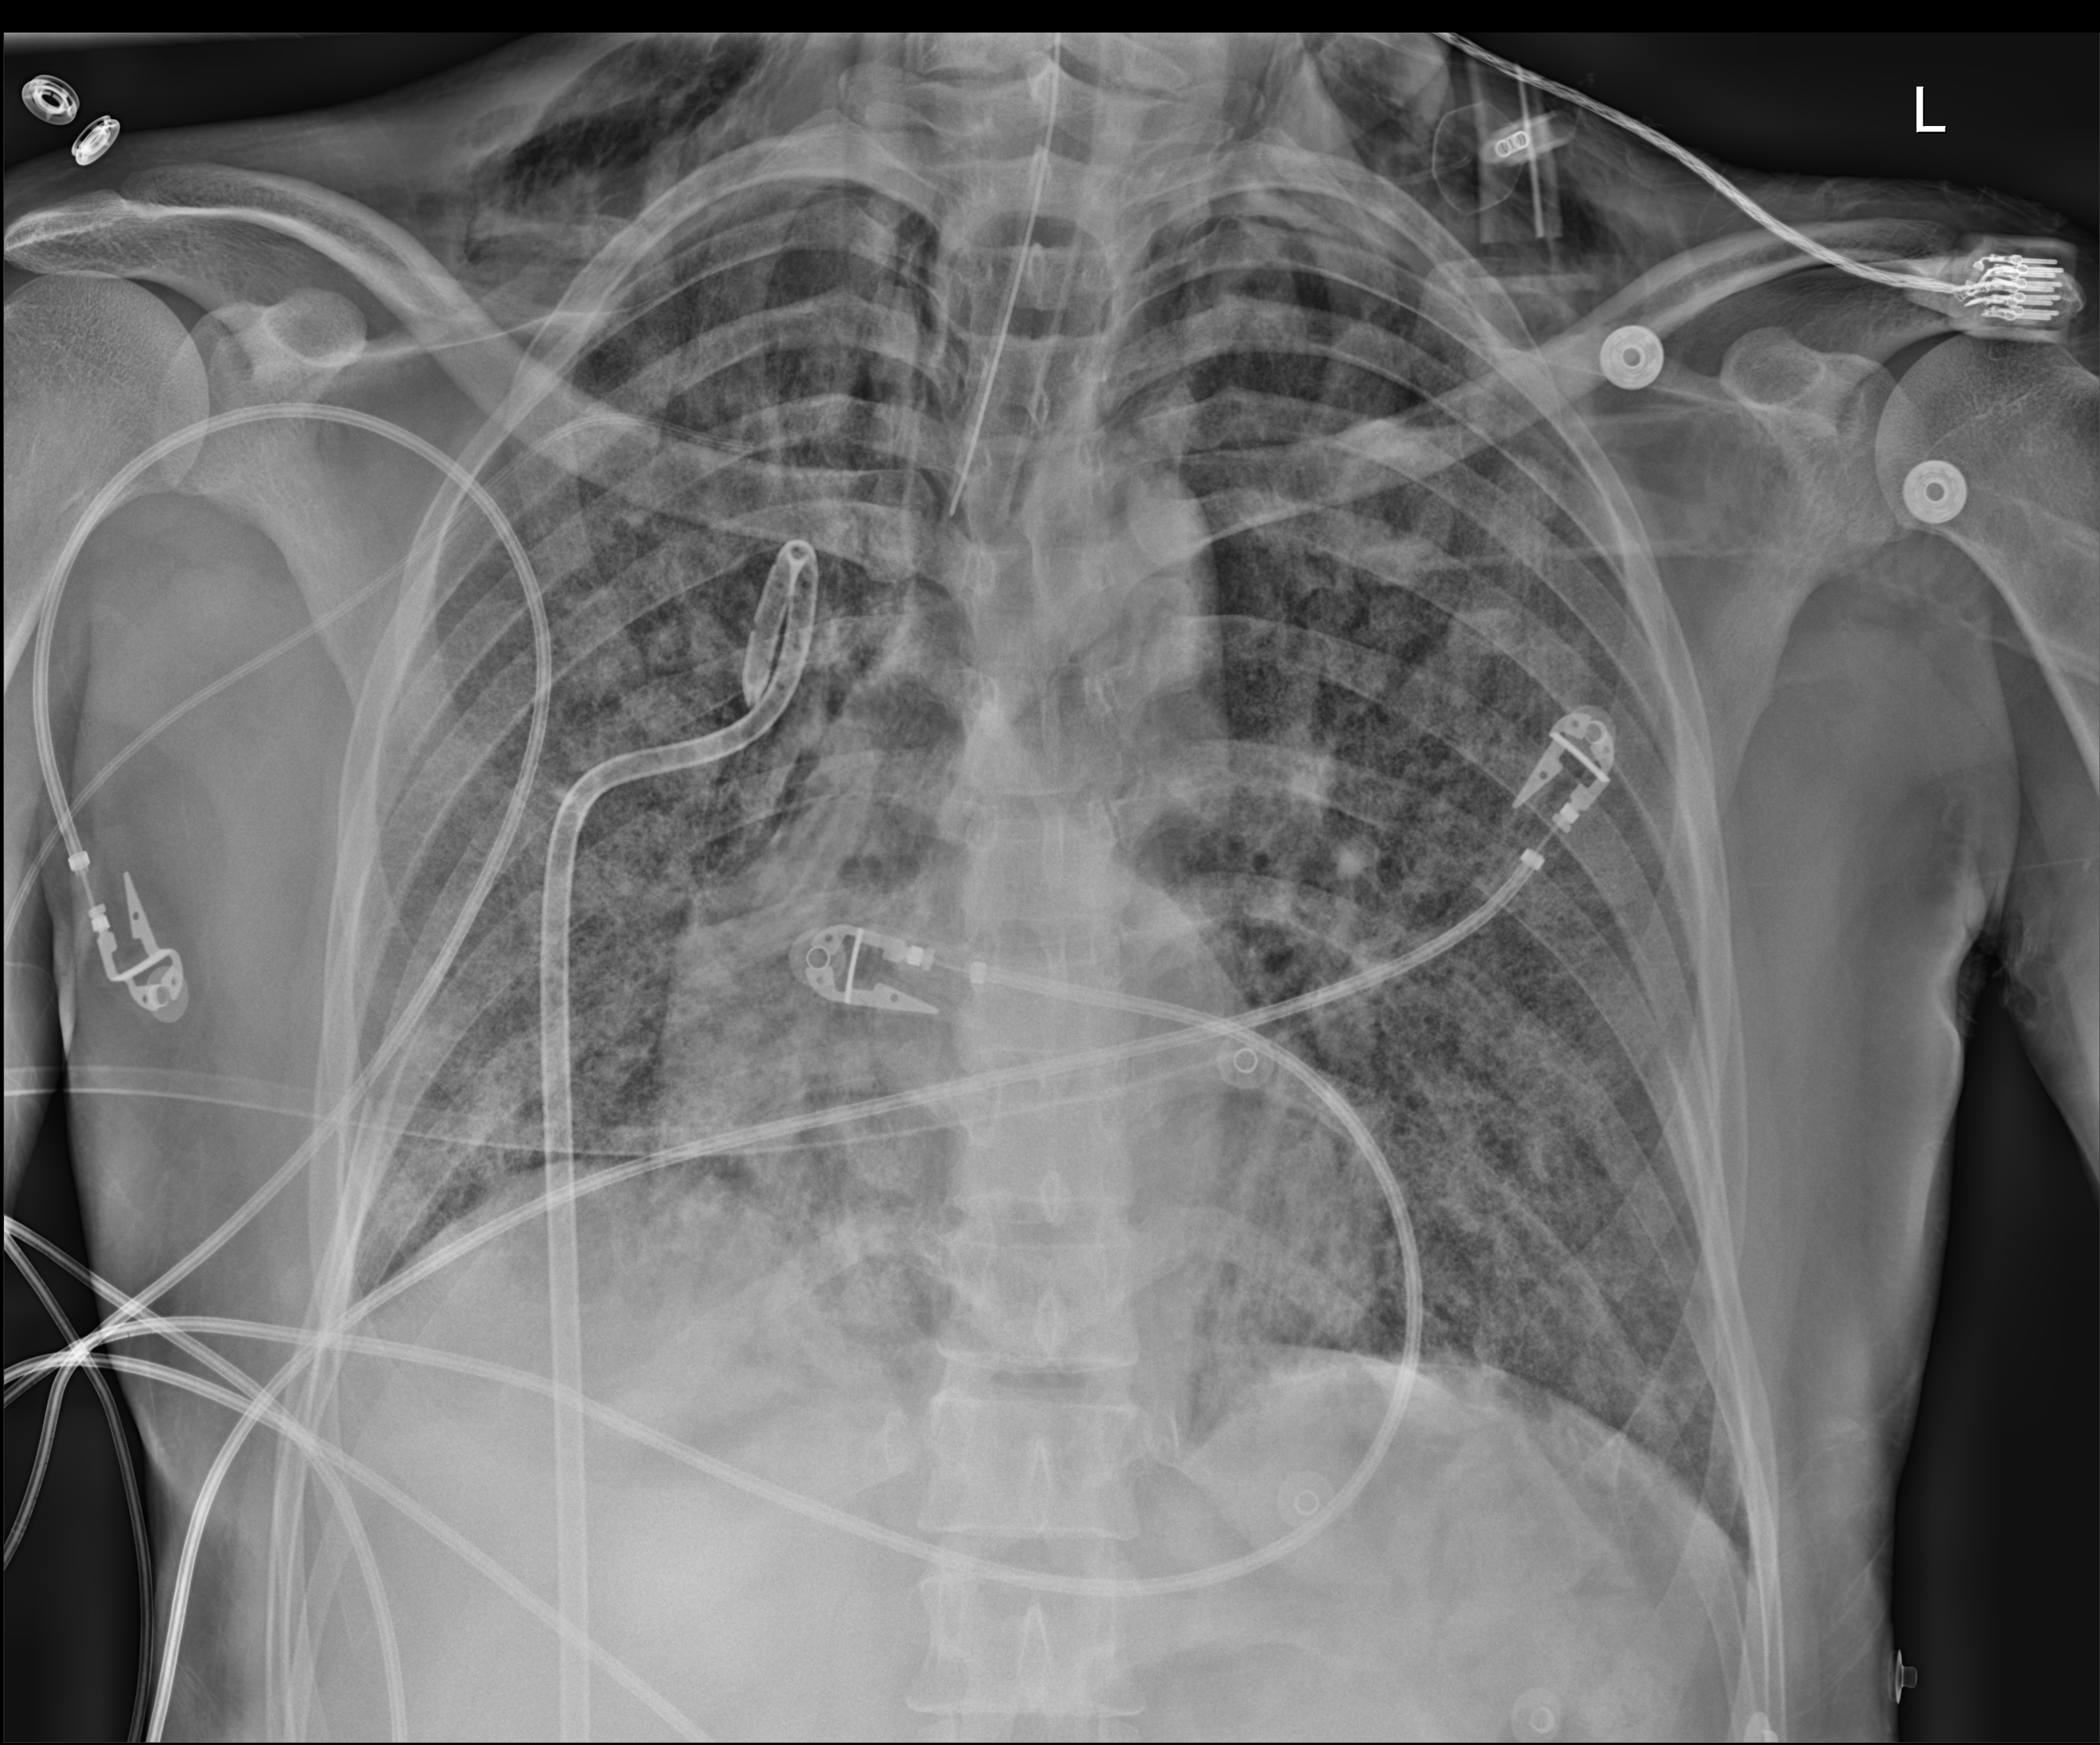
Portable chest radiograph, anteroposterior (AP) projection. Patient hospitalised with COVID-19, aged 18–59 years.
Hospital-stay facts (about this admission, not read from this image; timing relative to this image not recorded): mechanically ventilated during this hospital stay: yes.